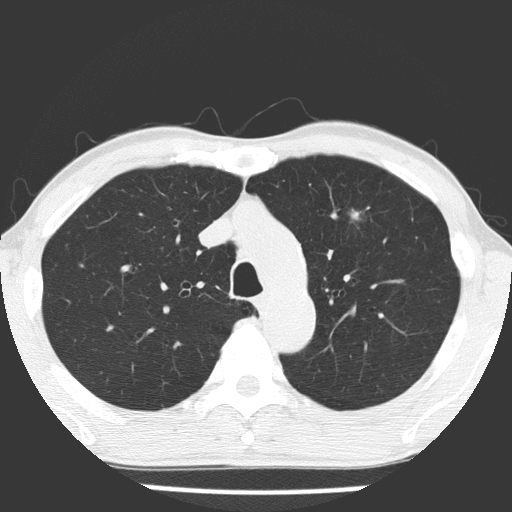
Low-dose screening chest CT, one axial slice; slice 126 of 177 in the series (ordered by position); lung window (W 1500 / L -600 HU); 2 mm slice thickness; 512 × 512 image matrix.
Structures marked on this image (outlined manually by an expert reader):
- lesion 1 (tumor, upper lobe of left lung): bounding box <348,208,366,224> (left, top, right, bottom; pixels)